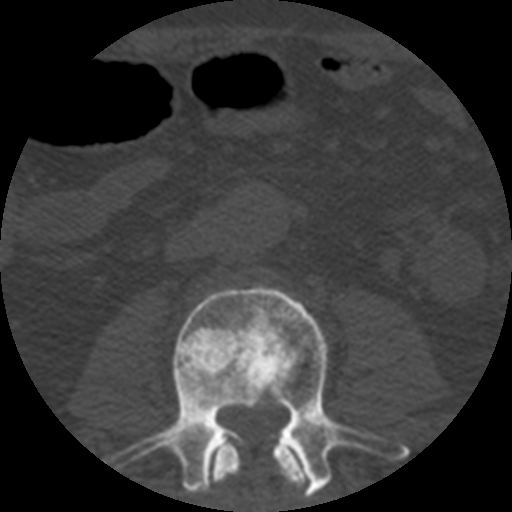
CT including the spine, one axial slice; slice 128 of 508 in the series (ordered by position); 120 kVp; bone window (W 1800 / L 400 HU); 1.25 mm slice thickness; 512 × 512 image matrix, field of view 160 × 160 mm. Patient age 57 years. Case-level facts recorded for this patient, not image findings: primary cancer: prostate.
Annotated regions visible in this slice (semi-automatic segmentation, software-assisted and operator-edited):
- L2 vertebra: bounding box [x1, y1, x2, y2] px = [209, 434, 310, 498]
- L3 vertebra: [104, 286, 409, 498]